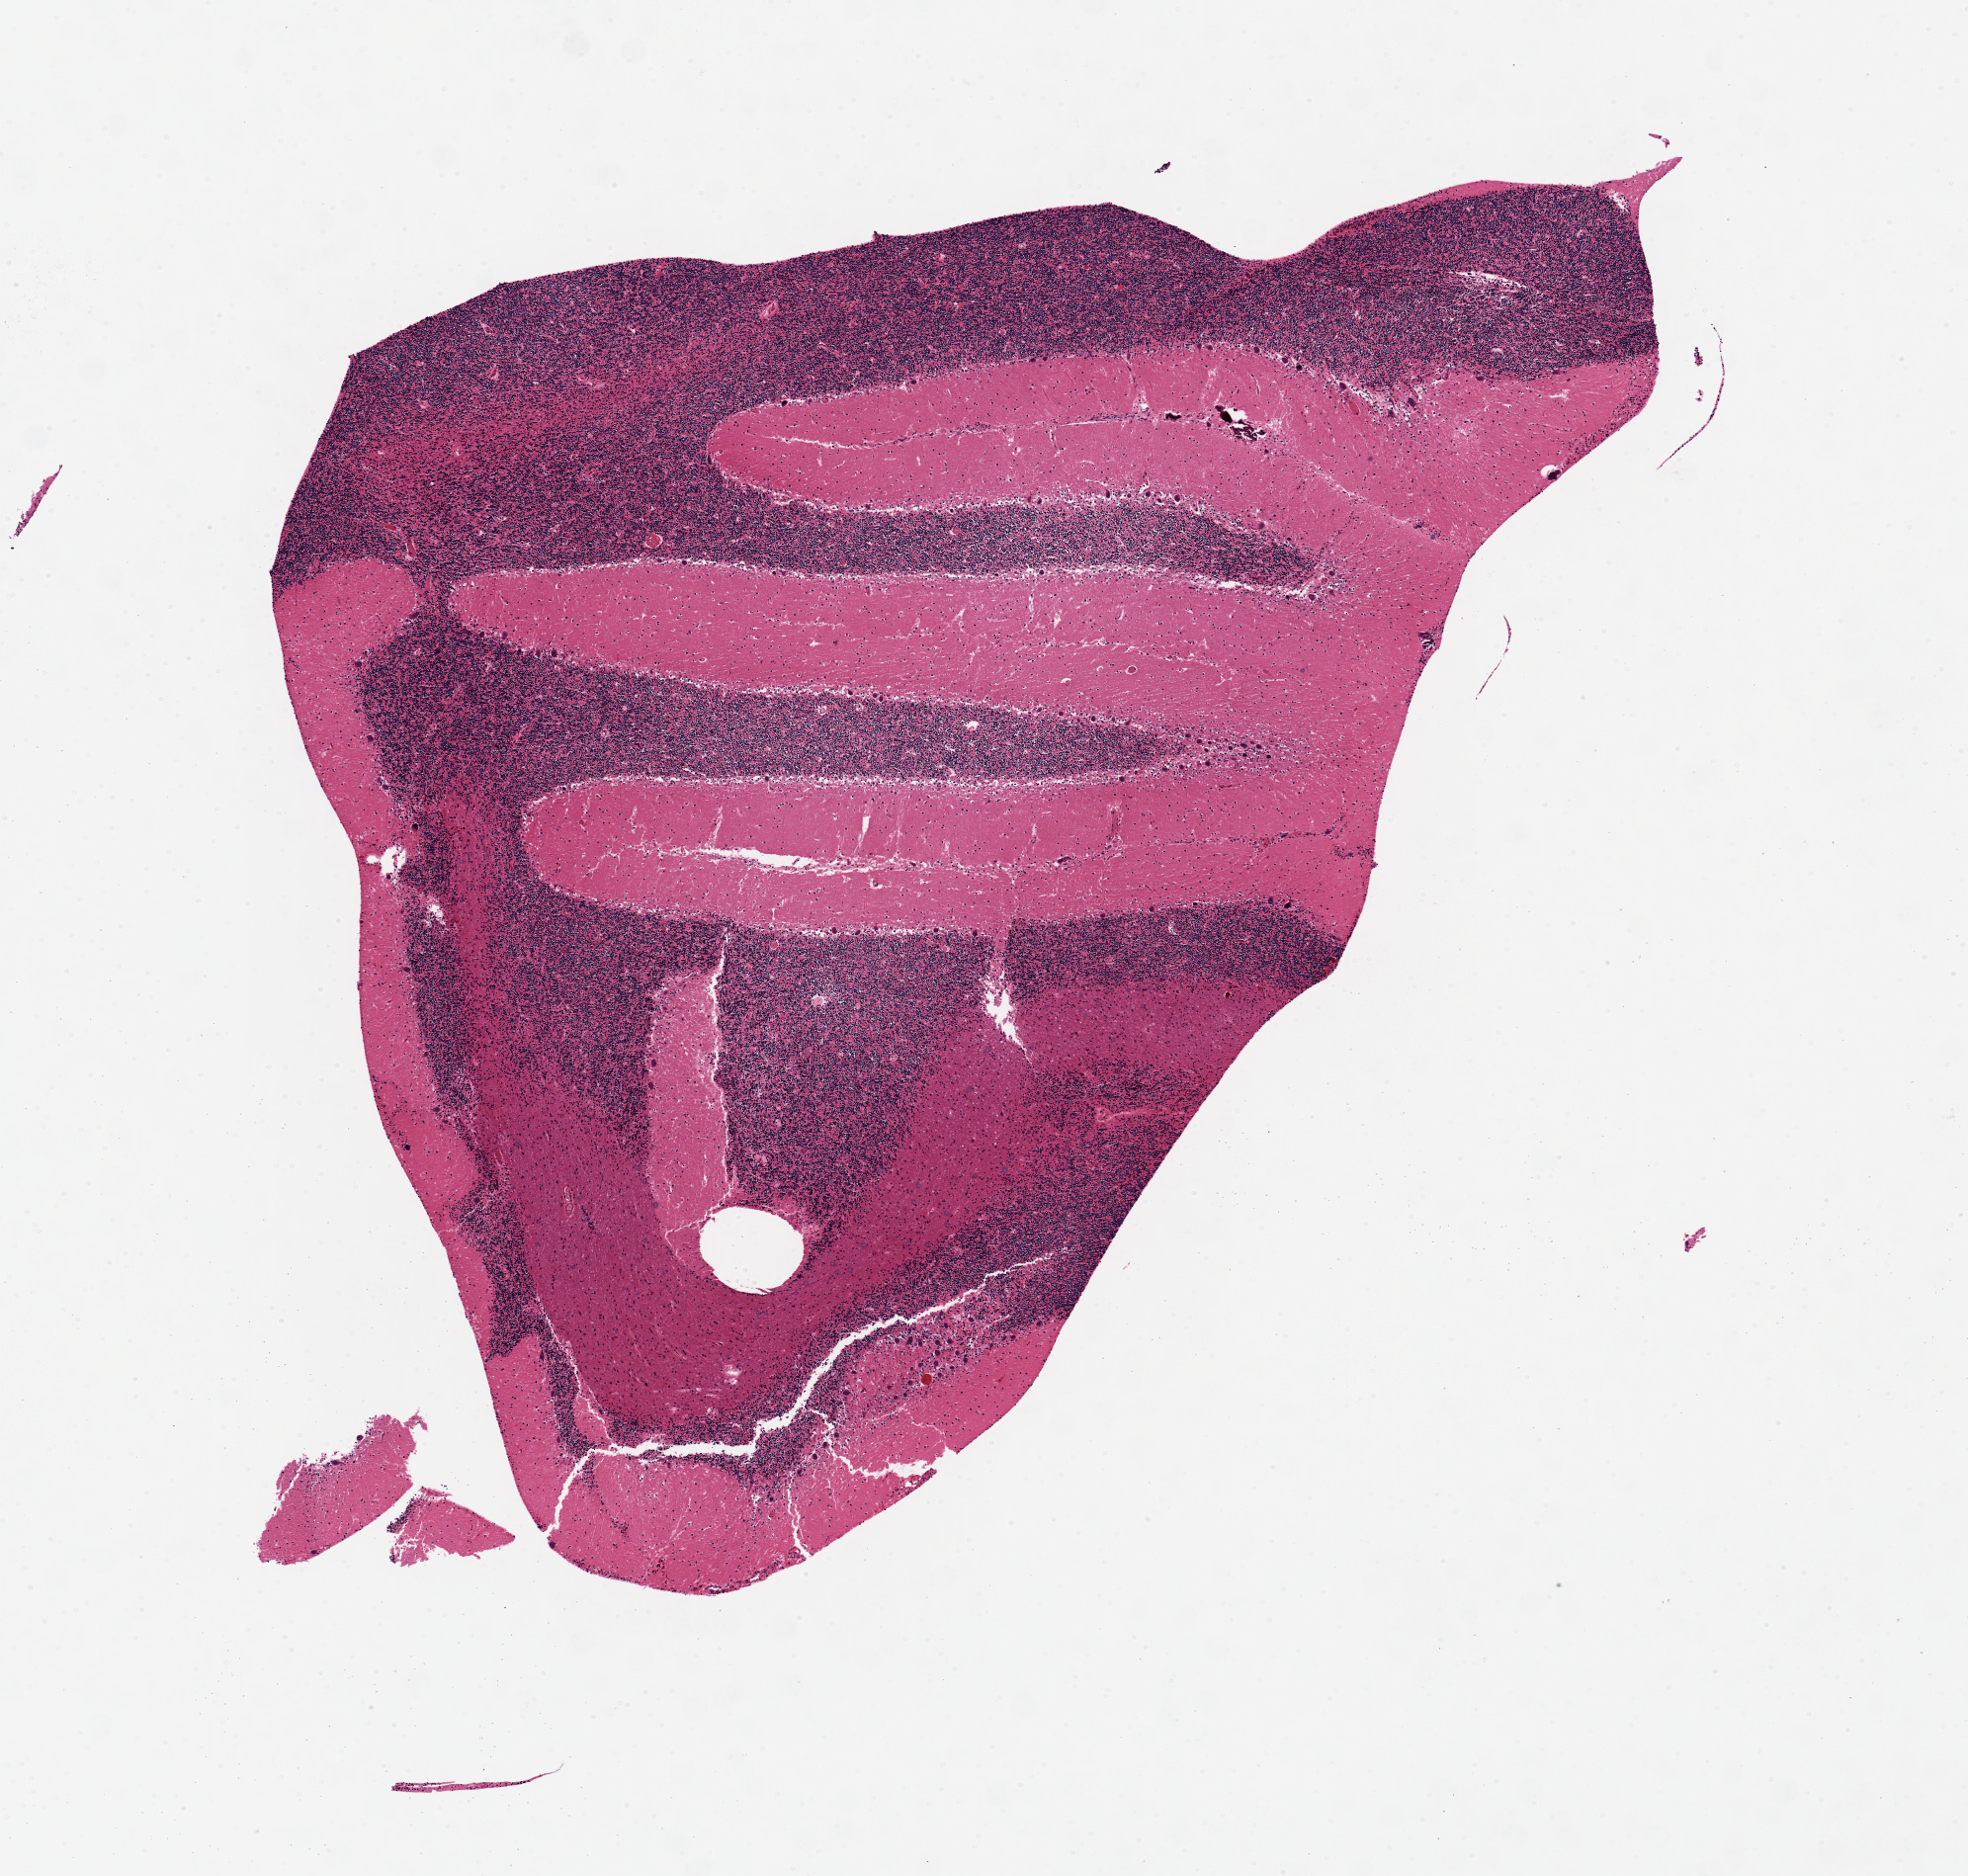
Digitized haematoxylin and eosin-stained section, brightfield — a low-resolution overview of the entire scanned area, about 7.9 x 7.5 mm (slide scanned at 20x); PAXgene-fixed paraffin-embedded (PFPE) section; section of cerebellum (target tissue); tissue donor sample.
Review note (as recorded): 4.5x6.8 Areas of poor fixation.